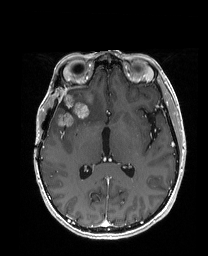
Brain MRI from a brain-tumour surgery series, one axial slice; T1-weighted post-contrast; 1 mm slice thickness; 208 × 256 image matrix, field of view 203 × 250 mm. From the clinical record (not read from this slice): histopathology: Metastatic Carcinoma from Breast primary; tumour location: Right Frontal.
Annotated regions visible in this slice (expert manual segmentation):
- previous resection cavity: box from (x=59, y=101) to (x=70, y=112) px
- tumour: (x=55, y=91)–(x=104, y=125)